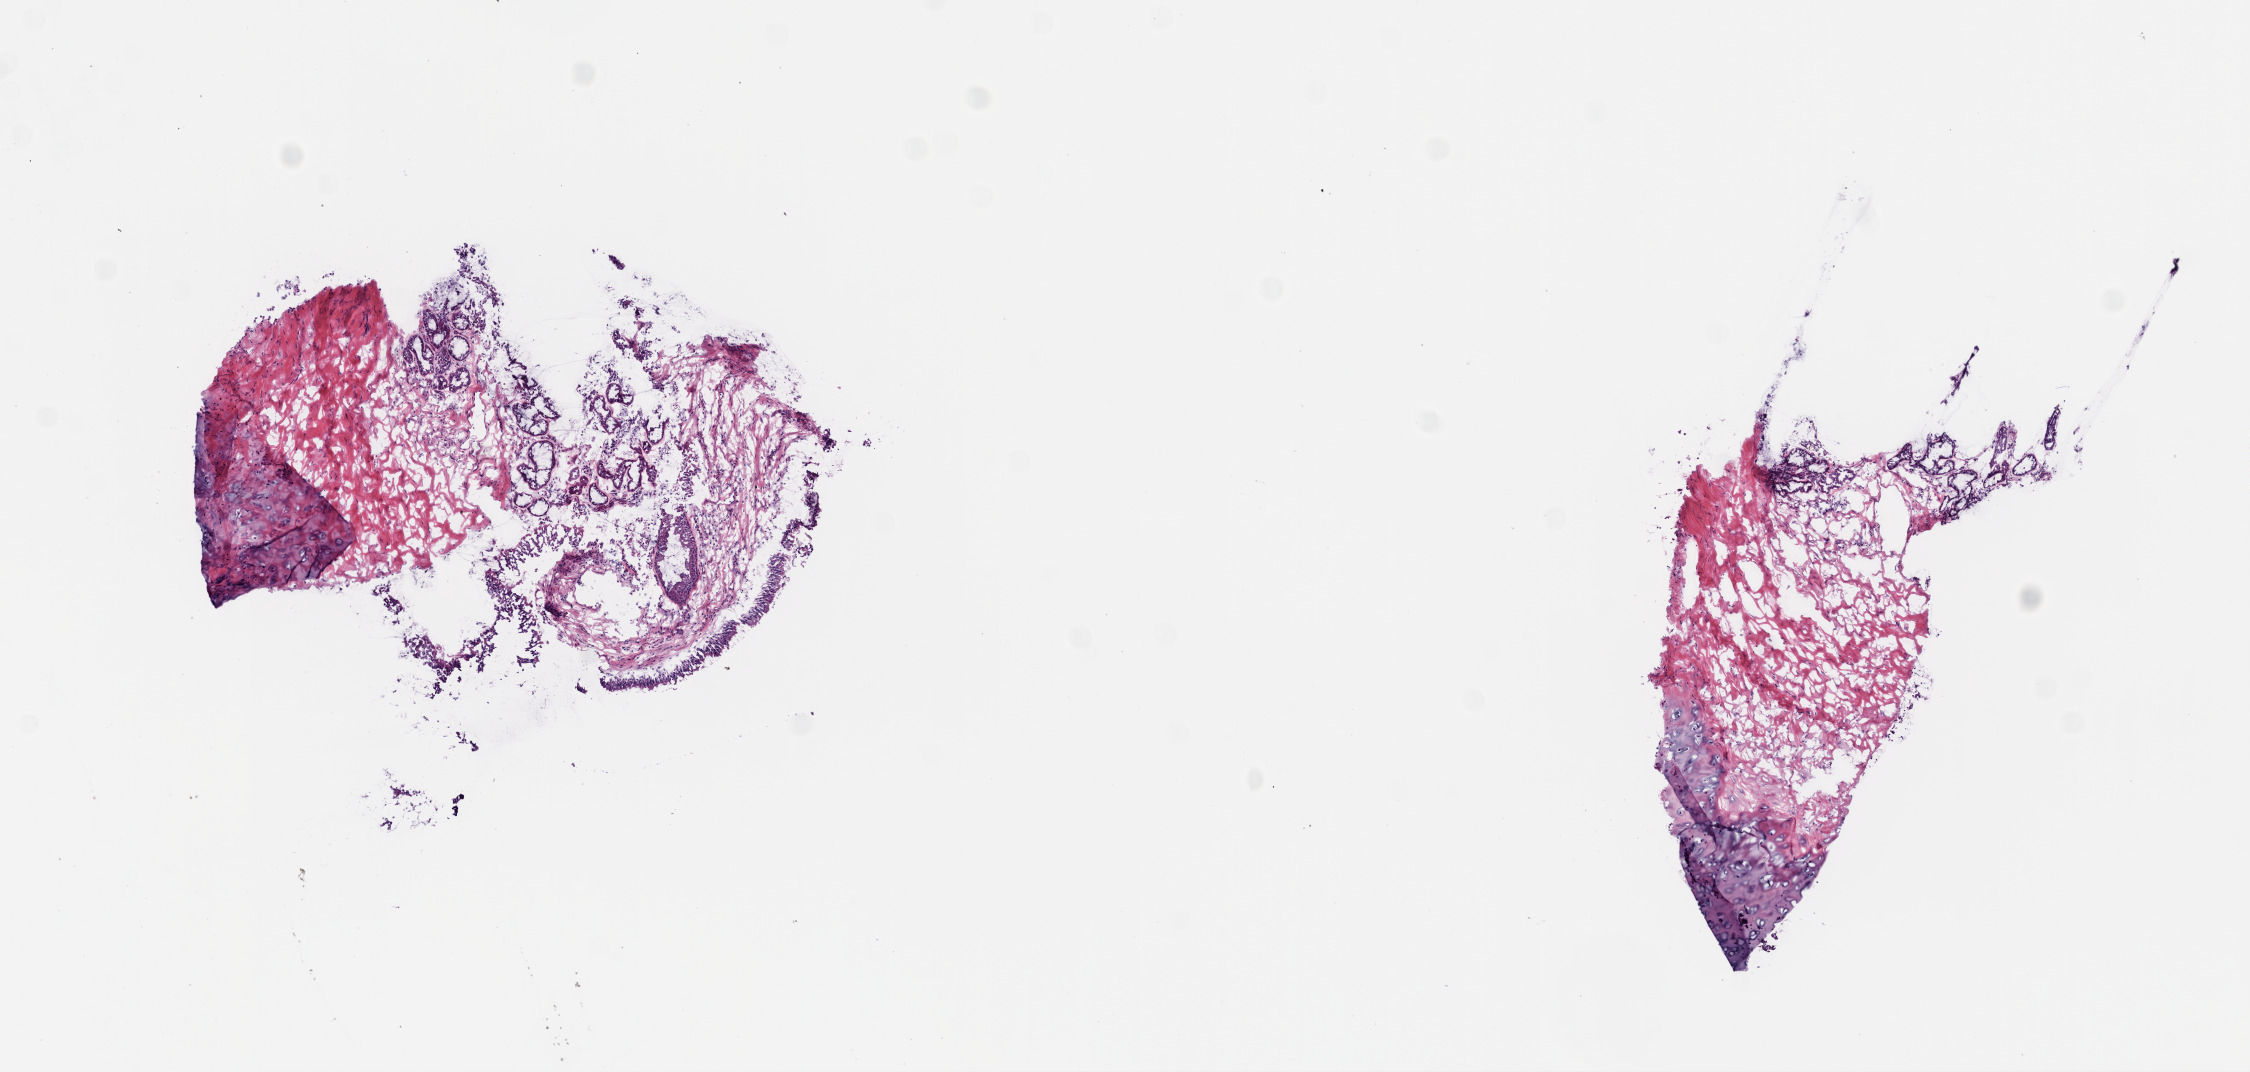
Whole-slide histology image, H&E-stained, a low-resolution overview of the entire scanned area, about 9.0 x 4.3 mm, frozen section from the top of the tissue portion, sample: solid tissue normal (non-tumour tissue), lung. Male, age 73 years at initial diagnosis.
This section: solid tissue normal sample (biorepository sample class). Patient diagnosis: Squamous cell carcinoma, NOS (lower lobe, lung).